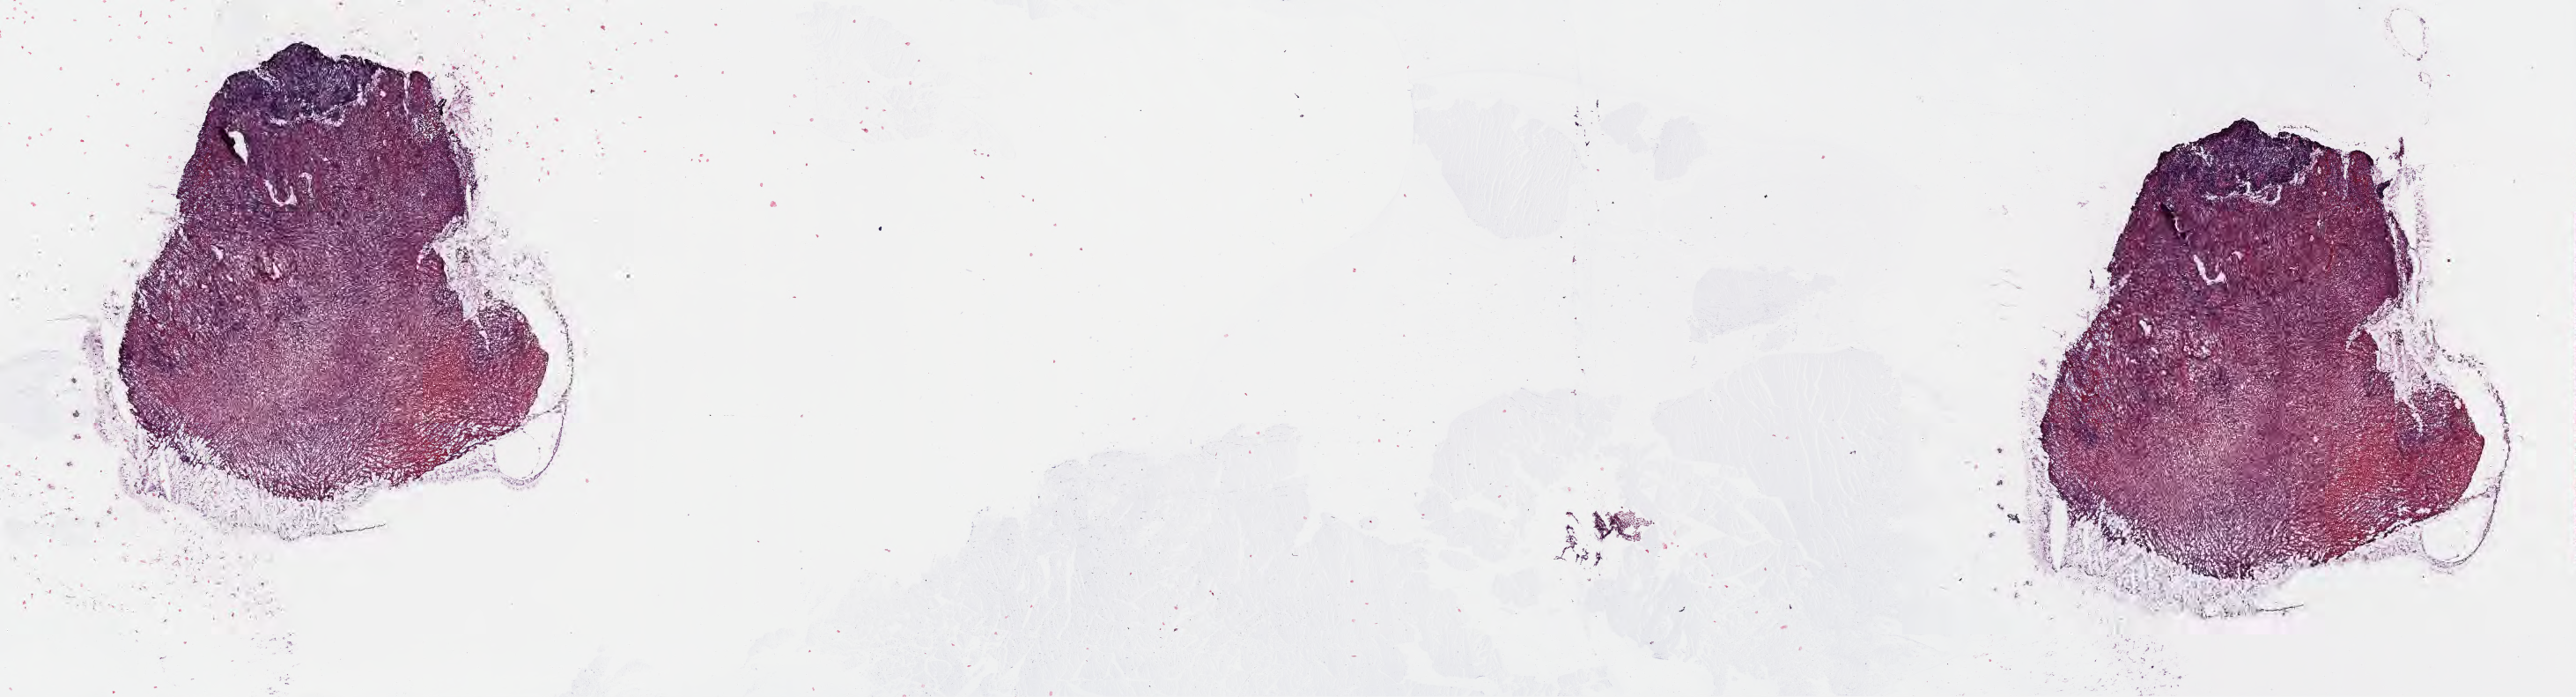
Whole-slide image, hematoxylin and eosin (H&E) stain, low-resolution overview of the scanned area, about 23.7 x 6.4 mm. Frozen section. Specimen: primary tumor. Site: mandible. Female, age 7 years at initial diagnosis. Pathologist review of this section (percent, as recorded): tumor cells 10%, tumor nuclei 30%, stromal cells 10%, necrosis 0%, normal cells 80%. Inflammatory infiltration, as recorded: lymphocyte infiltration 60%, monocyte infiltration 20%, neutrophil infiltration 5%.
* section: top of the tissue portion
* Ann Arbor stage (patient): Stage IV
* diagnosis: Burkitt lymphoma, NOS